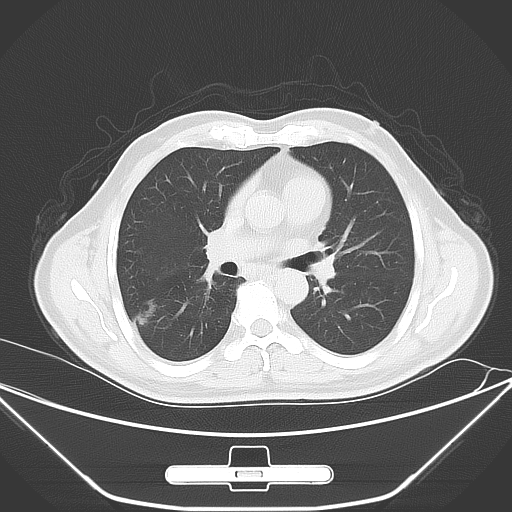
Chest CT, one axial slice. Slice 32 of 62 in the series (ordered by position). Lung window (W 1500 / L -600 HU). 512 × 512 image matrix, field of view 398 × 398 mm. Male patient, age 71 years. From the clinical record (not read from this slice): clinical TNM (as recorded): T1c N0 M0; histopathological grade: G2.
Structures marked on this image (bounding box drawn by a radiologist):
- lung tumour (recorded histology: adenocarcinoma): box from (x=131, y=300) to (x=166, y=328) px